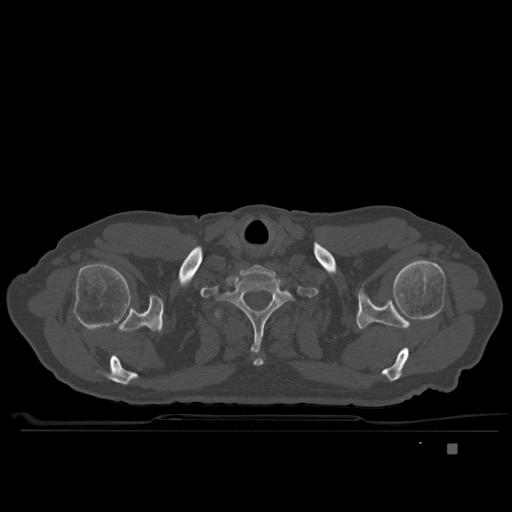
CT including the spine, one axial slice; position 324 of 435 along the scan axis; bone window (W 1800 / L 400 HU); 1.5 mm slice thickness; 512 × 512 image matrix, field of view 434 × 434 mm. Patient: male, 73 years. Case-level facts recorded for this patient, not image findings: primary cancer: skin.
Annotated regions visible in this slice (semi-automatic segmentation, software-assisted and operator-edited):
- T1 vertebra: bounding box <219,279,293,353> (left, top, right, bottom; pixels)
- T2 vertebra: <215,310,297,317>